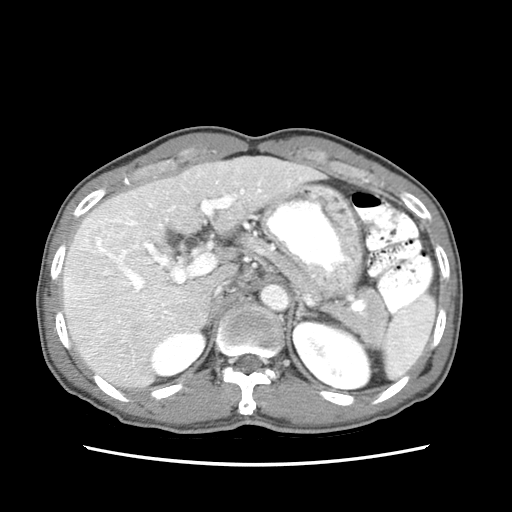
Contrast-enhanced abdominal CT (liver protocol), one axial slice; slice 44 of 79 in the series (ordered by position); reconstruction kernel STANDARD; 120 kVp; soft-tissue window (W 400 / L 40 HU); 512 × 512 image matrix, field of view 320 × 320 mm. Case-level facts recorded for this patient, not image findings: diagnosis: hepatocellular carcinoma (patient treated with transarterial chemoembolisation; whether this scan precedes or follows treatment is not stated here); TNM stage (as recorded): Stage-IIIB; Child-Pugh class: A; tumour differentiation: moderately differentiated; tumour nodularity: multinodular.
Structures marked on this image (semi-automatic segmentation, software-assisted and operator-edited):
- liver parenchyma outside the tumour (the mass and vessels are separate outlines, so this box may not span the whole liver): bounding box [x1, y1, x2, y2] px = [64, 154, 325, 390]
- mass: [63, 216, 133, 302]
- liver vessels: [98, 163, 311, 355]